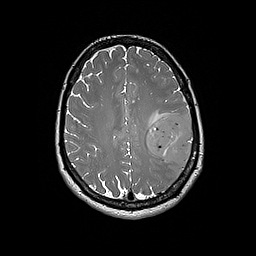
Brain MRI from a brain-tumour surgery series, one axial slice; position 73 of 192 along the scan axis; 1 mm slice thickness; 256 × 256 image matrix, field of view 250 × 250 mm. Case-level facts recorded for this patient, not image findings: histopathology: Glioblastoma; WHO grade: 4; IDH mutation: no; tumour location: Left Frontal.
Structures marked on this image (outlined manually by an expert reader):
- tumour: bounding box <146,113,194,165> (left, top, right, bottom; pixels)